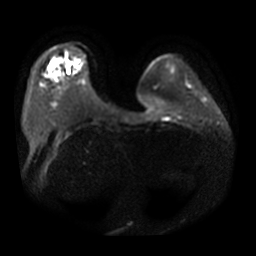
Breast MRI, one axial slice; position 8 of 31 along the scan axis; diffusion-weighted series; image 2 of 4 stored at this slice position (different b-values; order by instance number); 3 T; 5 mm slice thickness; 256 × 256 image matrix, field of view 380 × 380 mm. Female patient.
Outlined on this slice (expert manual segmentation):
- tumour on diffusion-weighted imaging: bounding box <51,60,60,67> (left, top, right, bottom; pixels)